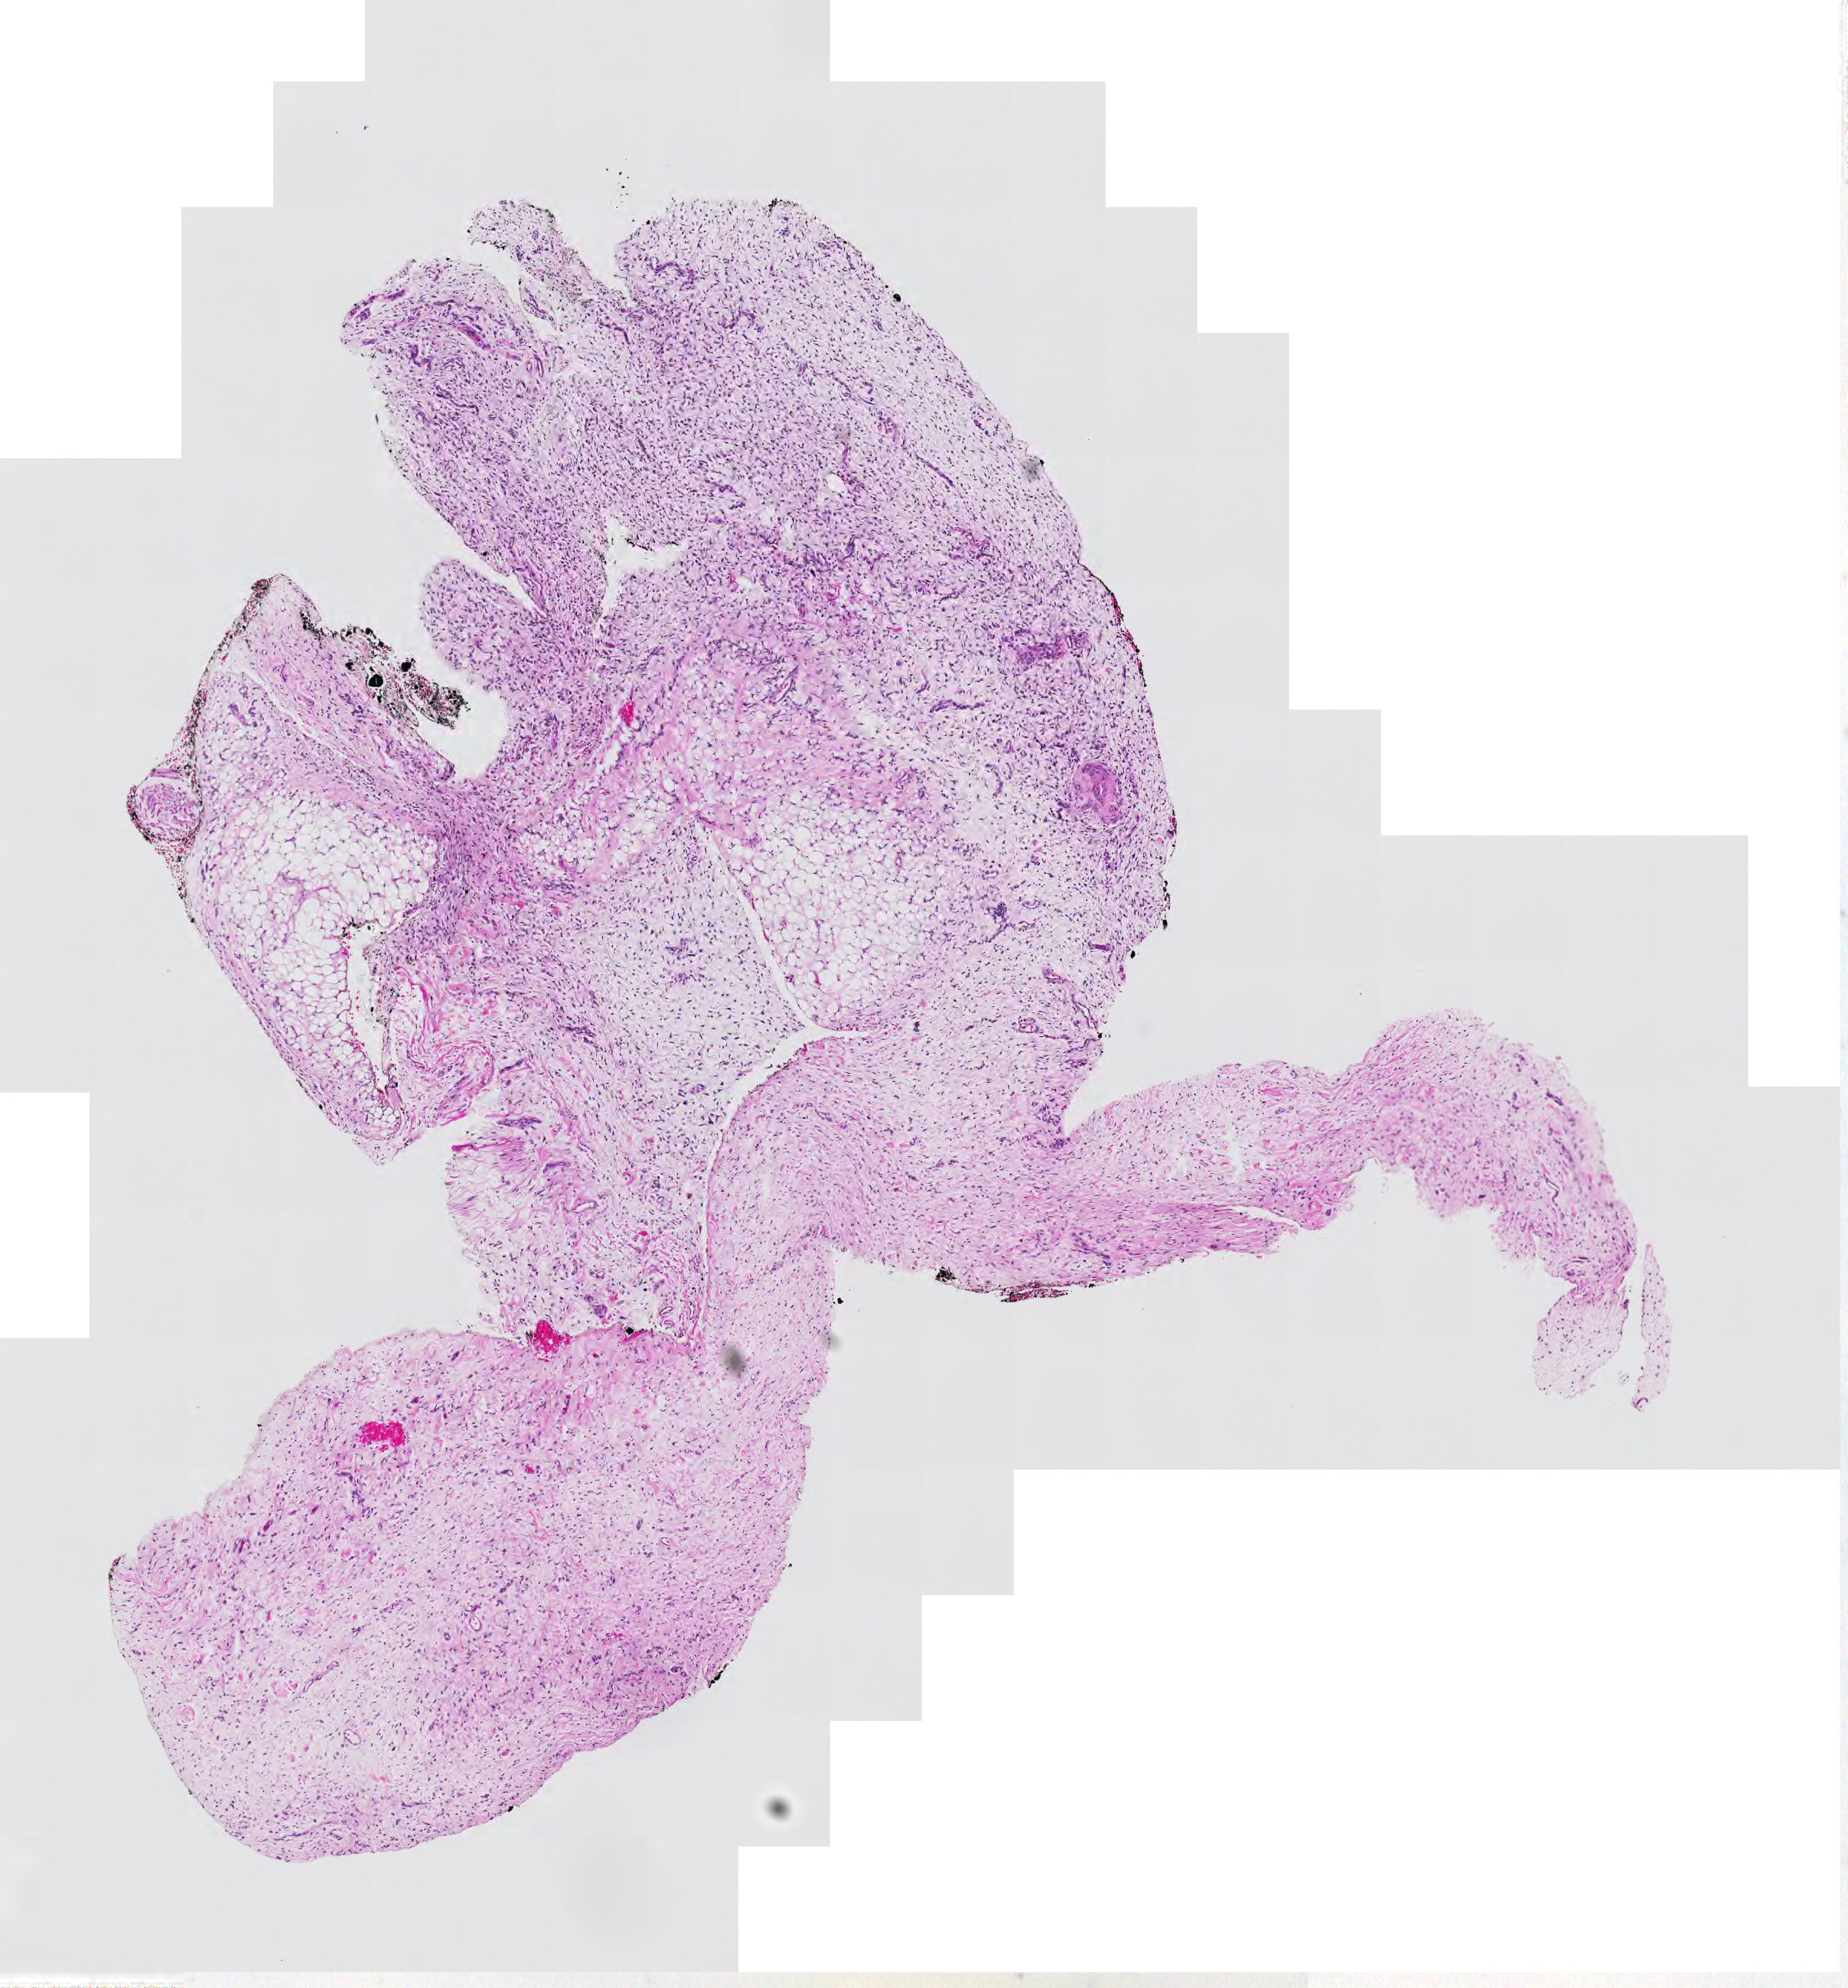
H&E whole-slide image, low-resolution overview of the scanned area, about 6.2 x 6.7 mm (acquisition: 20x scan); tumour tissue sample. Female, 72 y/o.
• patient diagnosis (cohort enrolment): sarcoma (site not recorded at cohort level)